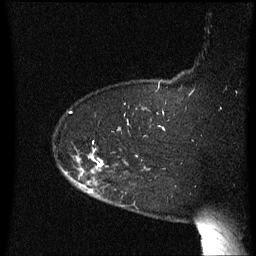
Breast MRI (dynamic contrast-enhanced), one sagittal slice; slice 51 of 60 in the series (ordered by position); dynamic contrast-enhanced series, image 2 of 3 at this slice position (ordered by acquisition); 1.5 T; TE 4.2 ms, TR 8.4 ms; 2.3 mm slice thickness; 256 × 256 image matrix, field of view 200 × 200 mm. Patient: female, 63 years. Case-level facts recorded for this patient, not image findings: setting: breast cancer imaged before/during neoadjuvant chemotherapy; receptor status: HER2-positive.
Outlined on this slice (semi-automatic segmentation, software-assisted and operator-edited):
- analysis volume of interest (the breast-tissue region the enhancement analysis was run in; not a lesion): bounding box <64,150,123,203> (left, top, right, bottom; pixels)
- tumour enhancement mask (voxels above the 70 % enhancement threshold inside the analysis volume of interest): <90,156,102,191>